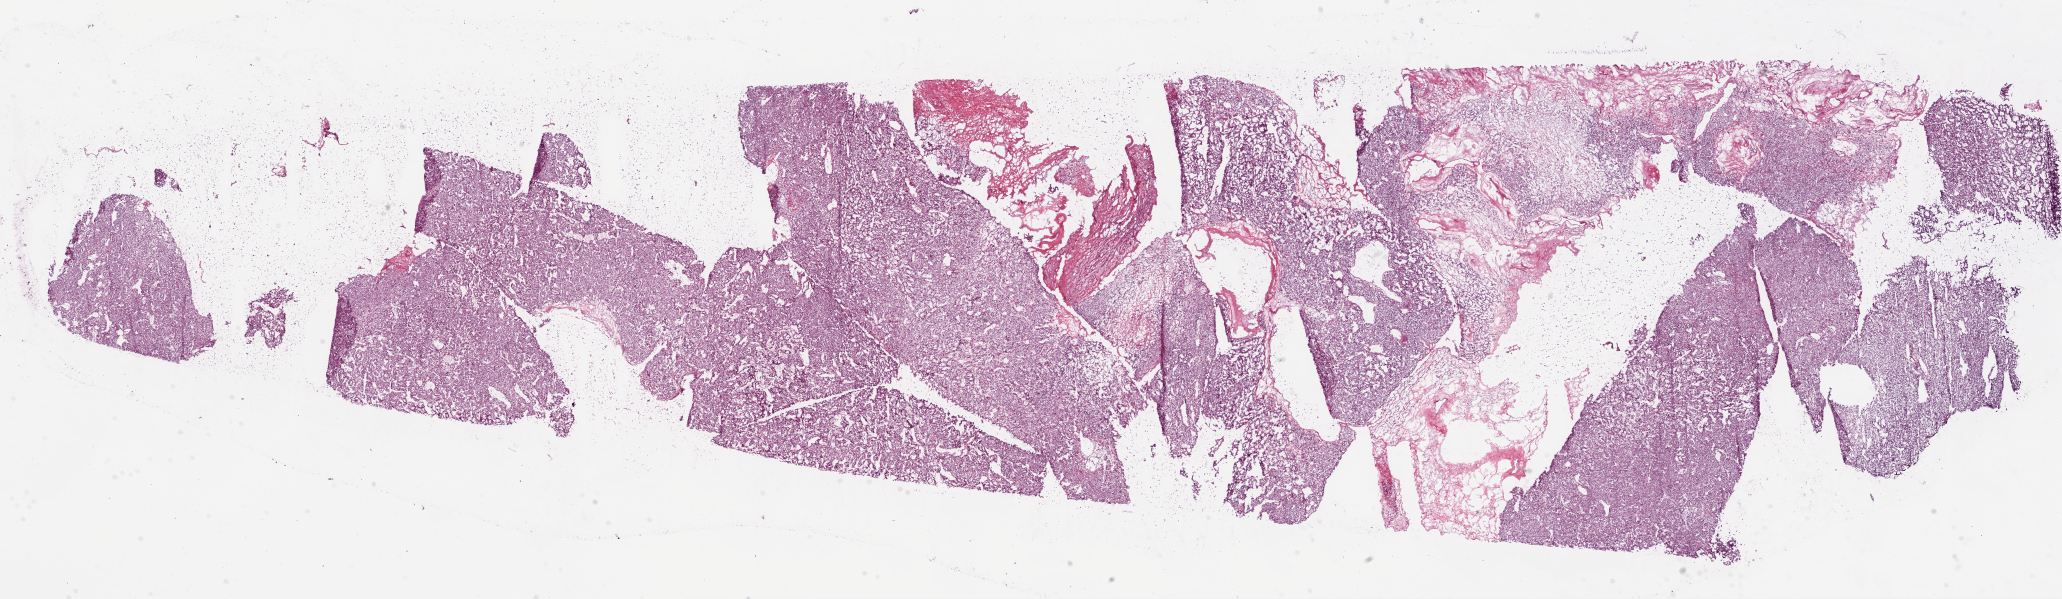
Whole-slide histology image, H&E-stained — whole scanned area (about 33.1 x 9.6 mm) shown as a low-resolution overview; frozen section; sample: primary tumour, kidney. Male, age 64 years at initial diagnosis. Histologic grade: G3 (poorly differentiated). Slide review estimates, as recorded: tumour cells 85%, tumour nuclei 85%, normal cells 0%, stromal cells 15%, necrosis 0%.
Histologic diagnosis: Clear cell adenocarcinoma, NOS. AJCC pathologic stage: IV (7th edition). TNM: T3a NX M1.